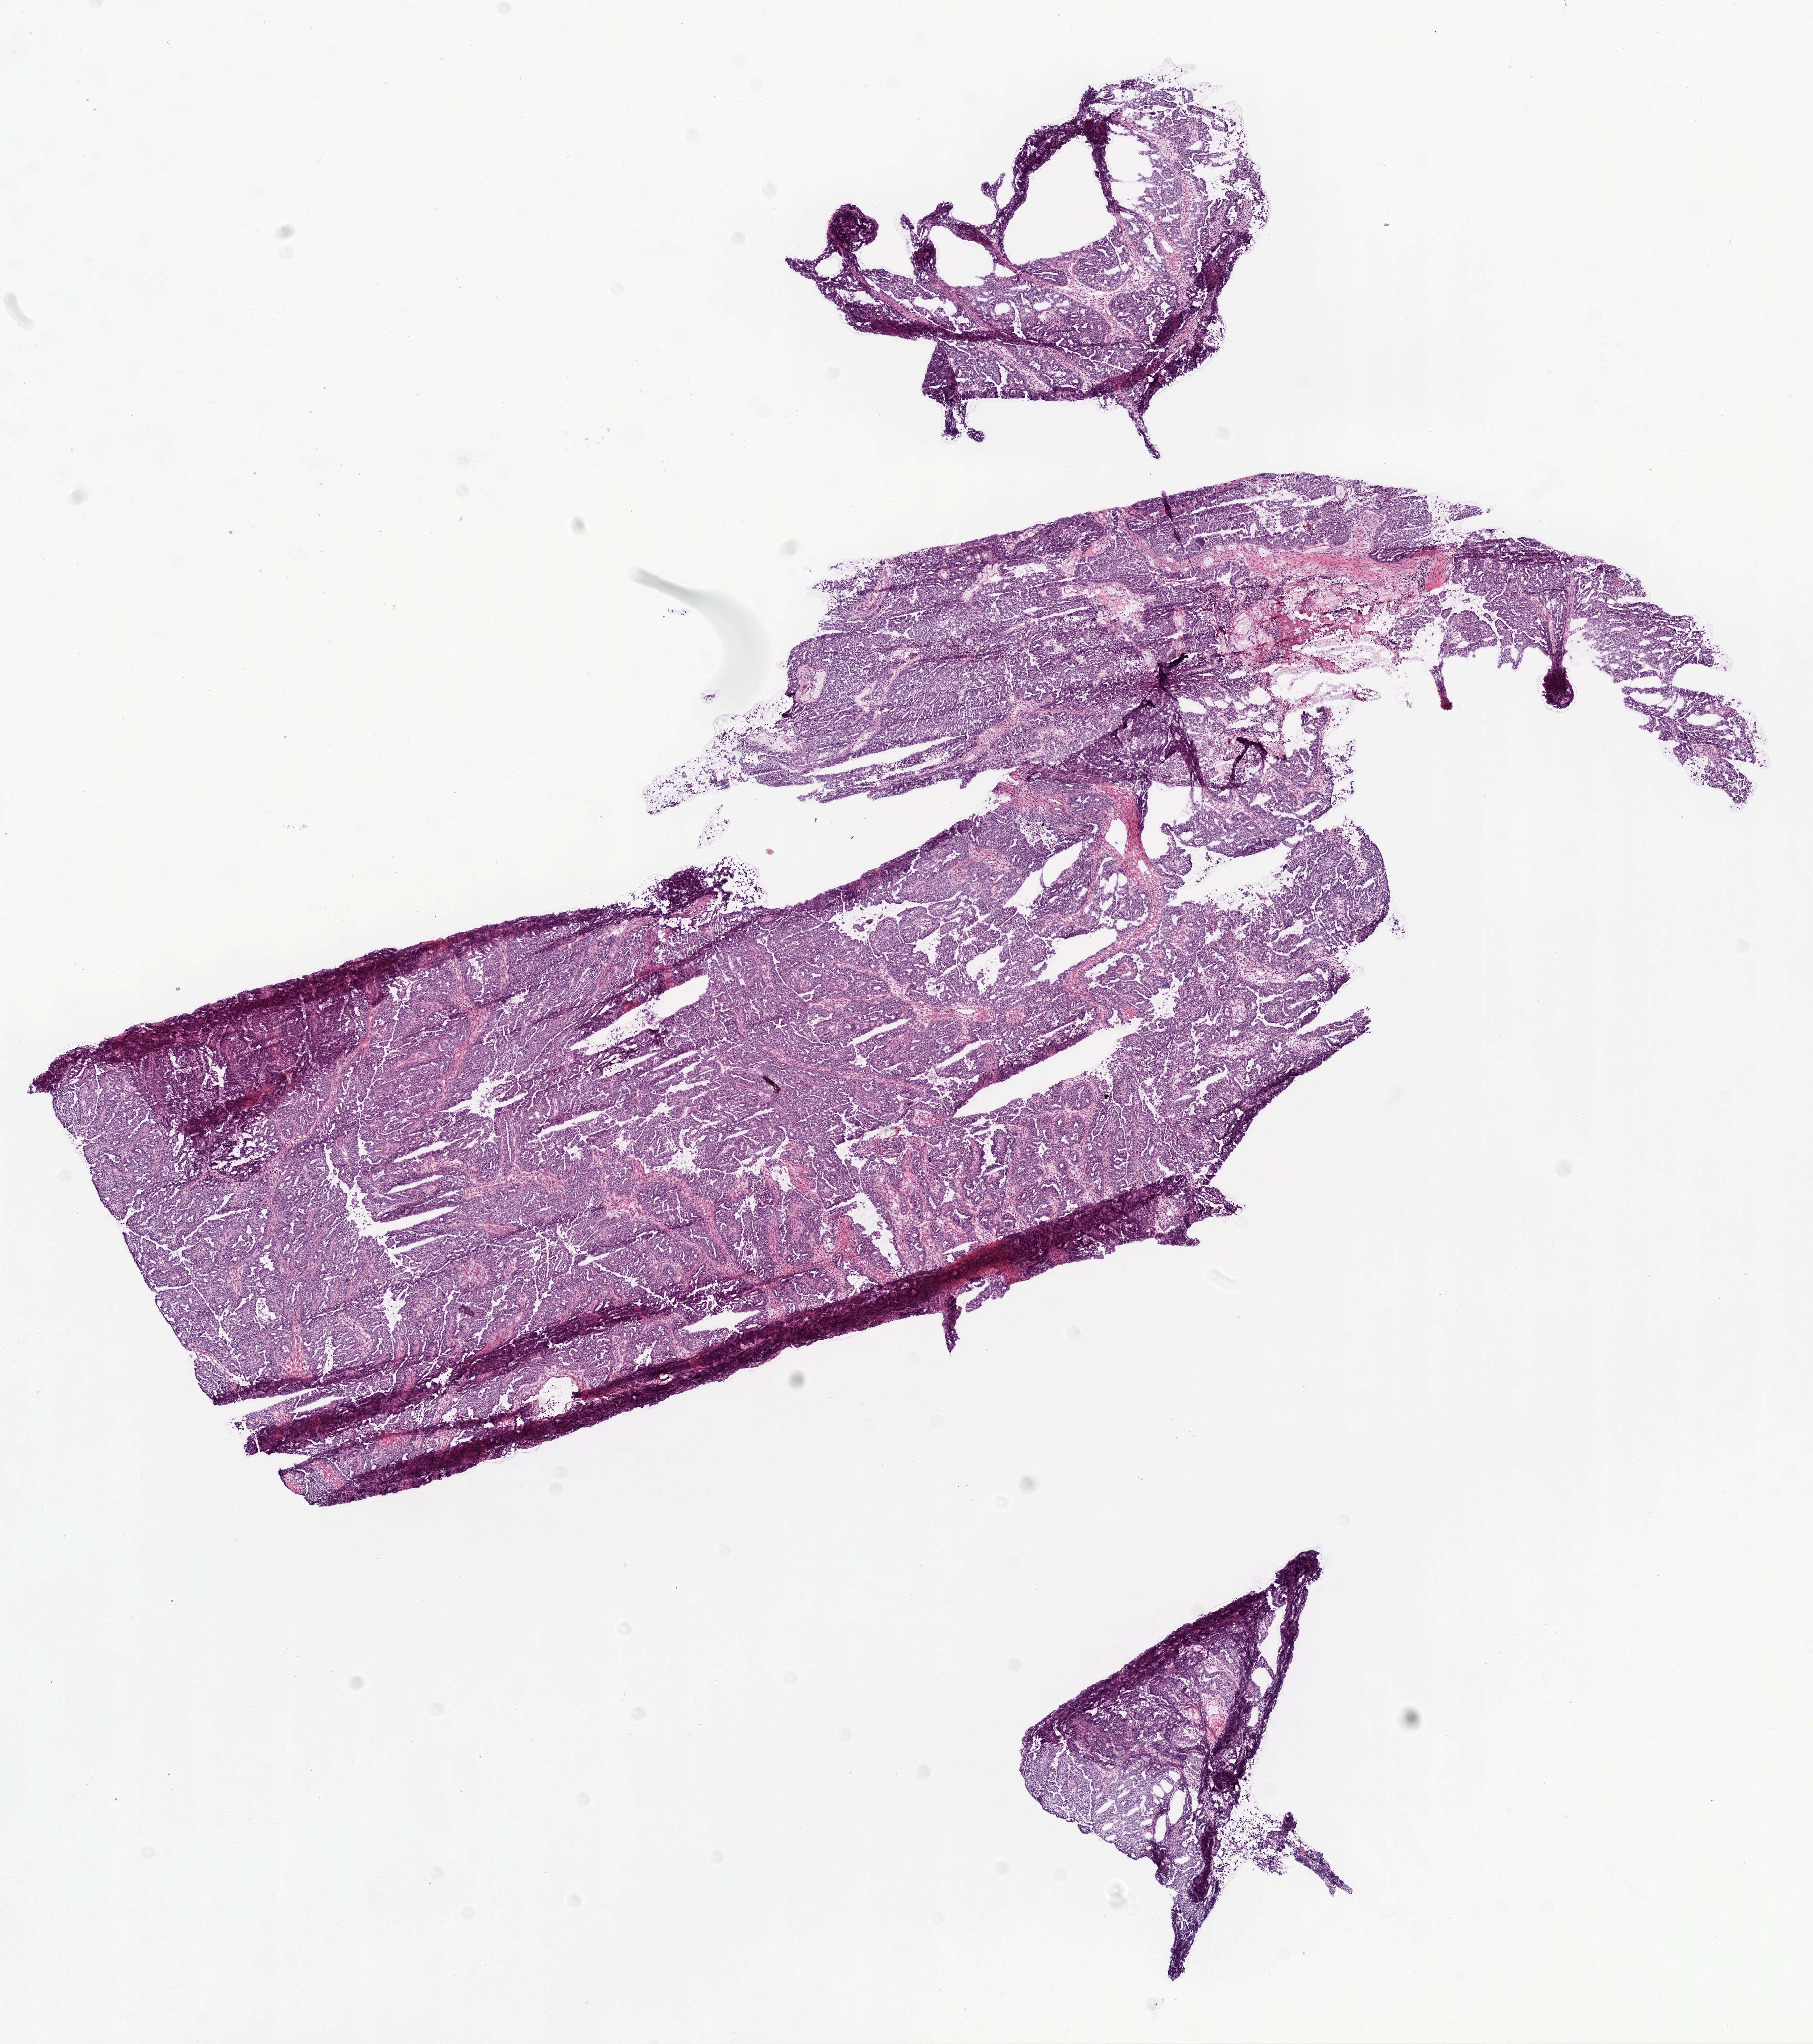
Digitized Hematoxylin and eosin (H&E) stained tissue section (whole slide) — low-resolution overview of the scanned area, about 11.0 x 12.4 mm (slide scanned at 20x). Frozen section from the top of the tissue portion. Sample: primary tumour, ovary. Female patient; age at initial diagnosis 49 years. Histologic grade: G3 (poorly differentiated). Pathologist review of this section (percent, as recorded): tumour cells 94%, tumour nuclei 95%, normal cells 0%, stromal cells 5%, necrosis 1%.
FIGO stage: IIIC. Laterality: bilateral. Histologic diagnosis: Serous cystadenocarcinoma, NOS.